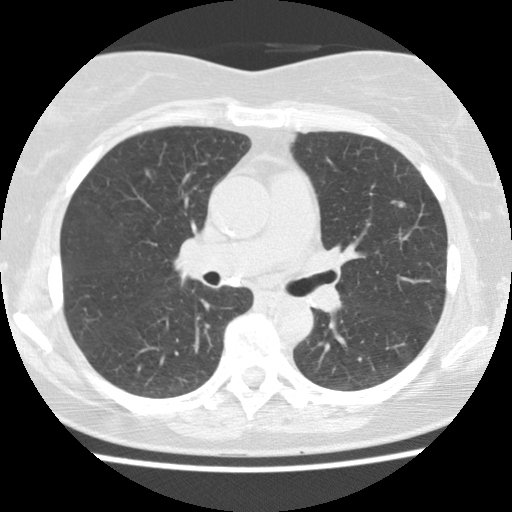
Axial slice from a low-dose chest CT screening exam, baseline annual screen, lung window (W 1500 / L -600 HU), 2.5 mm slice thickness, standard (soft-tissue) reconstruction kernel (STANDARD). Female participant, aged 60 years at enrolment. Current smoker at enrolment.
• Expert-annotated lung lesion, bounding box [x1, y1, x2, y2] px = [373, 188, 421, 224].
• The screening reader recorded 2 non-calcified nodules or masses ≥4 mm on this exam (left upper lobe, right upper lobe); which of them this box marks is not recorded.
• Official screen result: positive, change unspecified: nodule(s) >= 4 mm or enlarging nodule(s), mass(es), or other non-specific abnormalities suspicious for lung cancer.
• Participant outcome: lung cancer diagnosed 388 days after this screen — non-small cell carcinoma, left upper lobe, poorly differentiated (G3), stage IA (AJCC 6th edition), 10 mm at pathology.